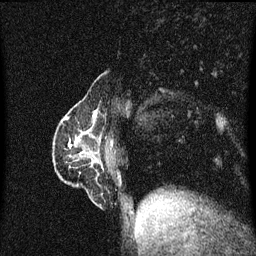
Breast MRI (dynamic contrast-enhanced), one sagittal slice. Slice 17 of 60 in the series (ordered by position). Dynamic contrast-enhanced series, image 2 of 3 at this slice position (ordered by acquisition). 1.5 T. TE 4.2 ms, TR 8.4 ms. 256 × 256 image matrix. Female patient, age 40 years.
Annotated regions visible in this slice (semi-automatically segmented with operator editing):
- analysis volume of interest (the breast-tissue region the enhancement analysis was run in; not a lesion): bounding box [x1, y1, x2, y2] px = [57, 110, 110, 191]
- tumour enhancement mask (voxels above the 70 % enhancement threshold inside the analysis volume of interest): [66, 118, 76, 149]